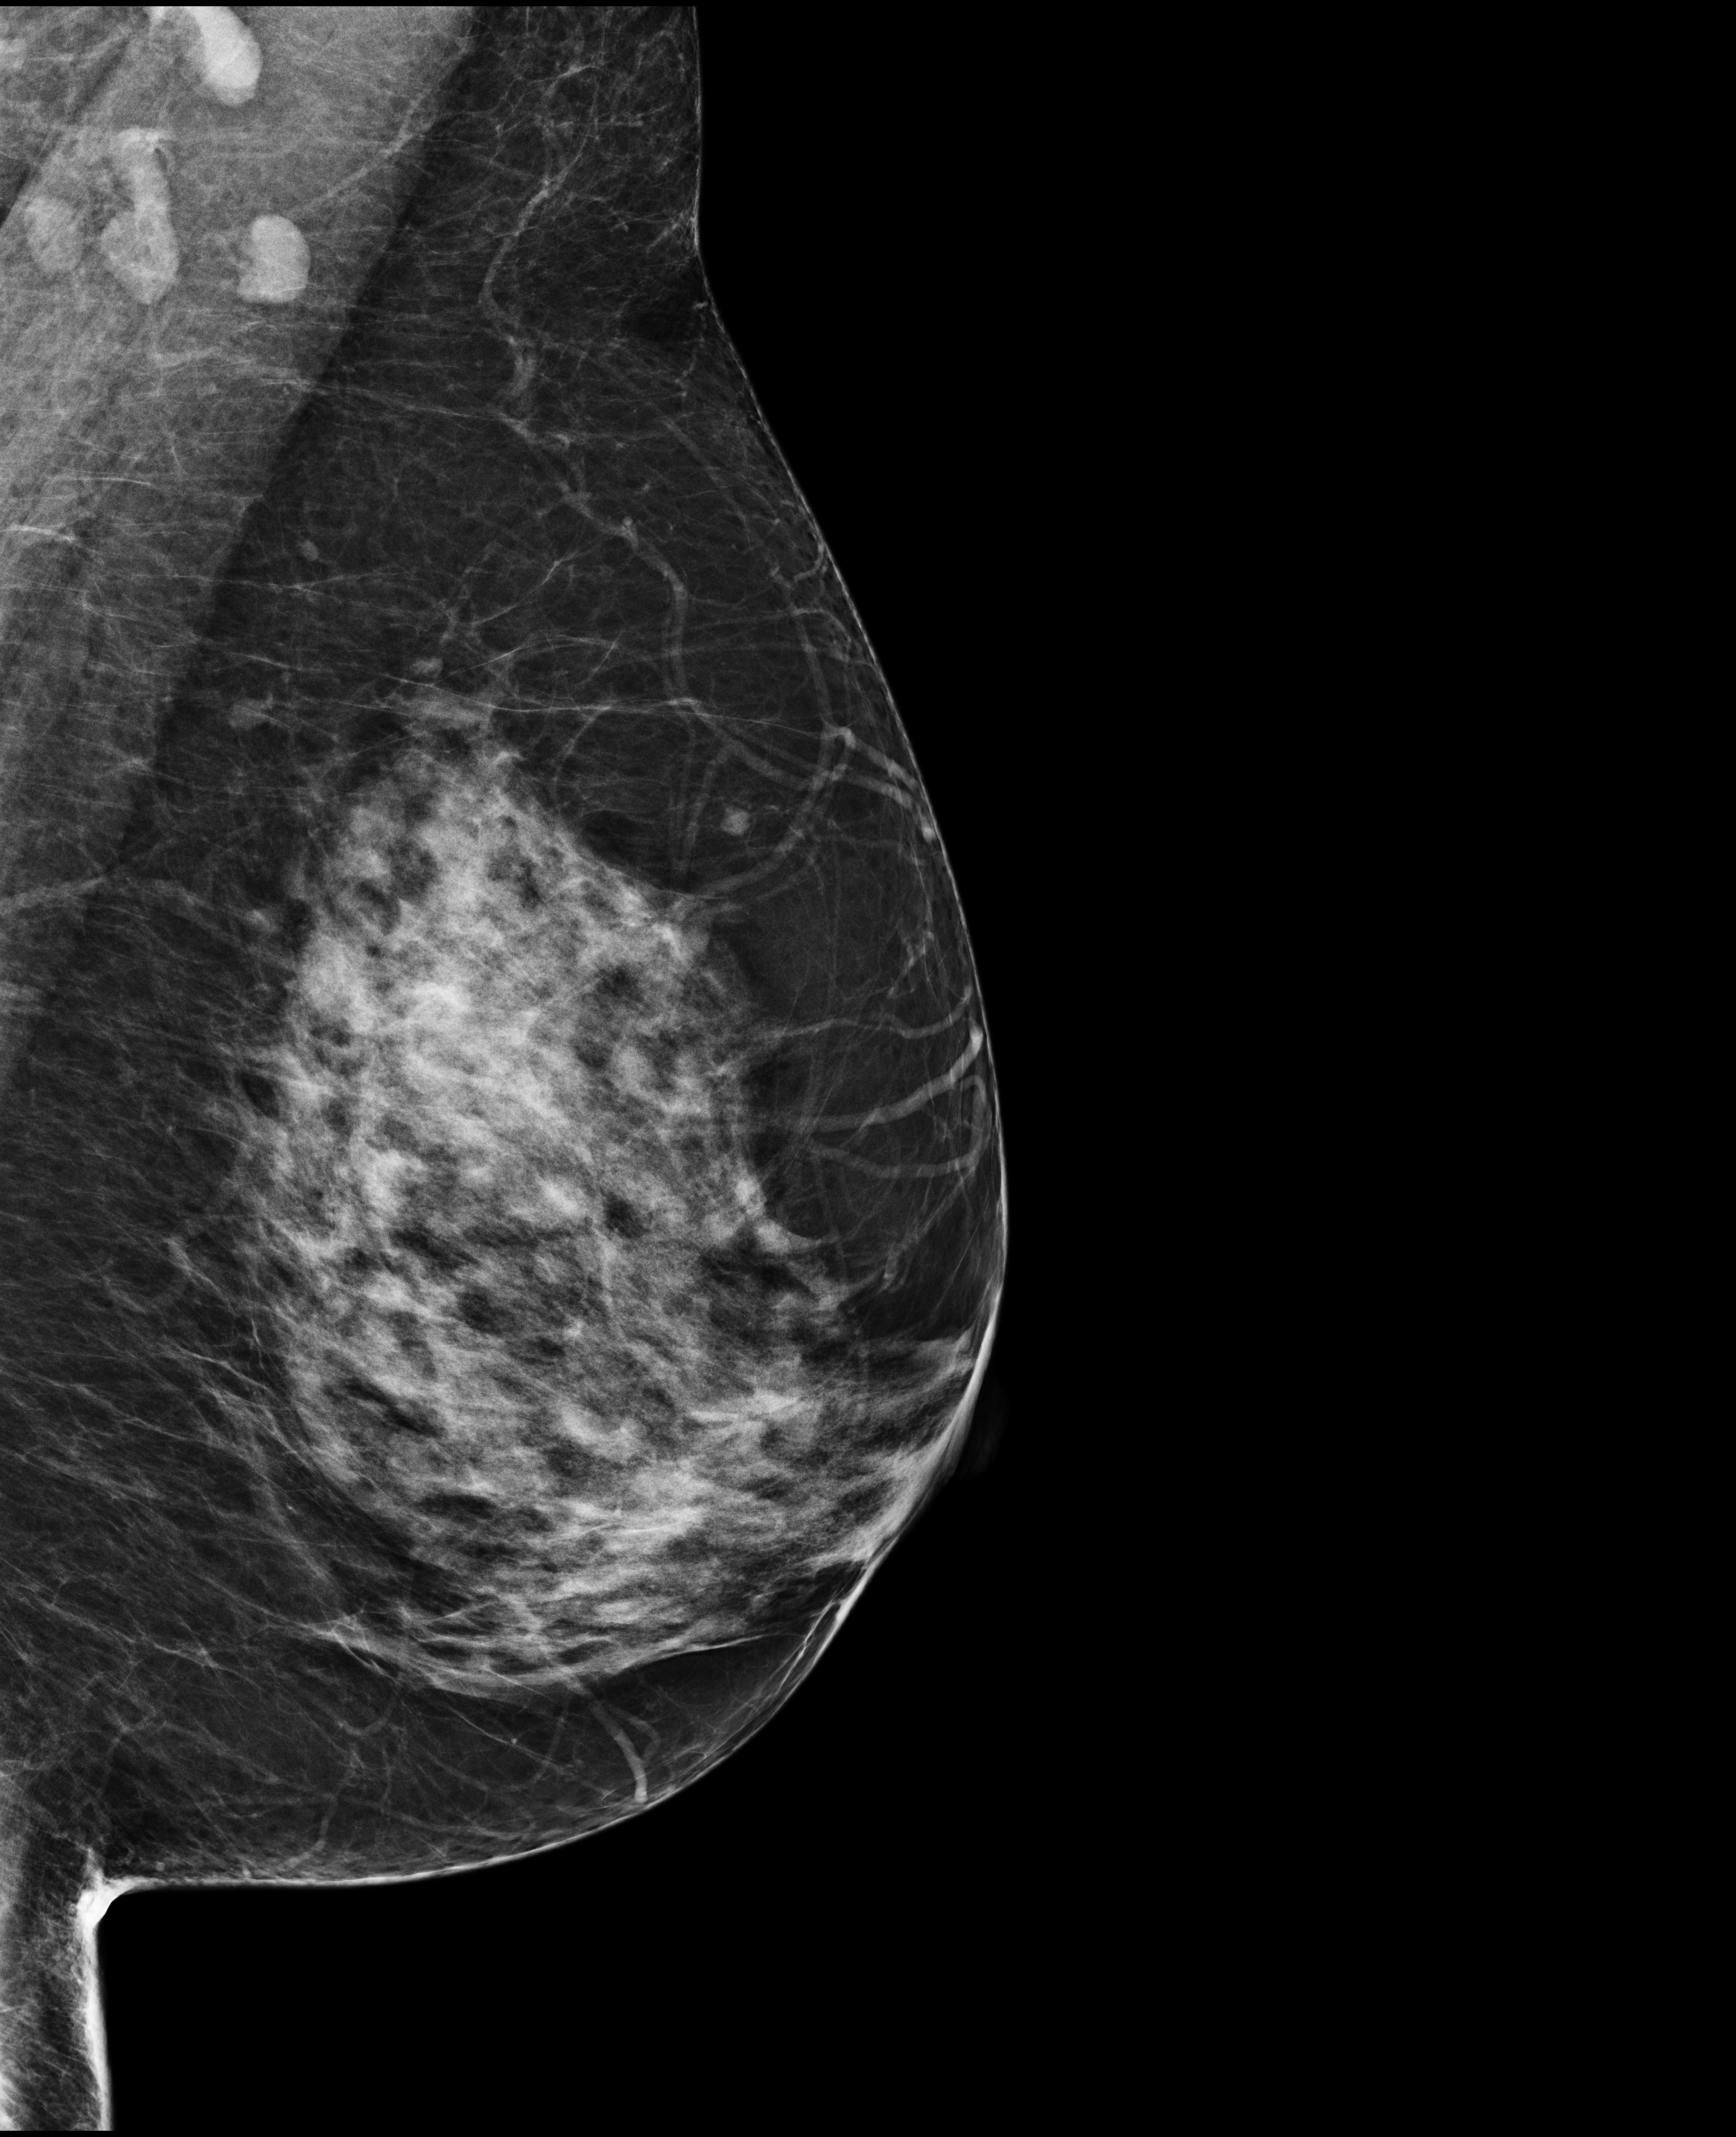
Digital mammogram (FFDM), left breast, mediolateral oblique (MLO) view, annual screening mammography examination. Patient aged 59 years (female).
Breast density at the screening exam (both breasts): heterogeneously dense (BI-RADS density category c). Final BI-RADS category for the screening round (tomosynthesis exam, both breasts): category 2. Recall: no recall after this screen.